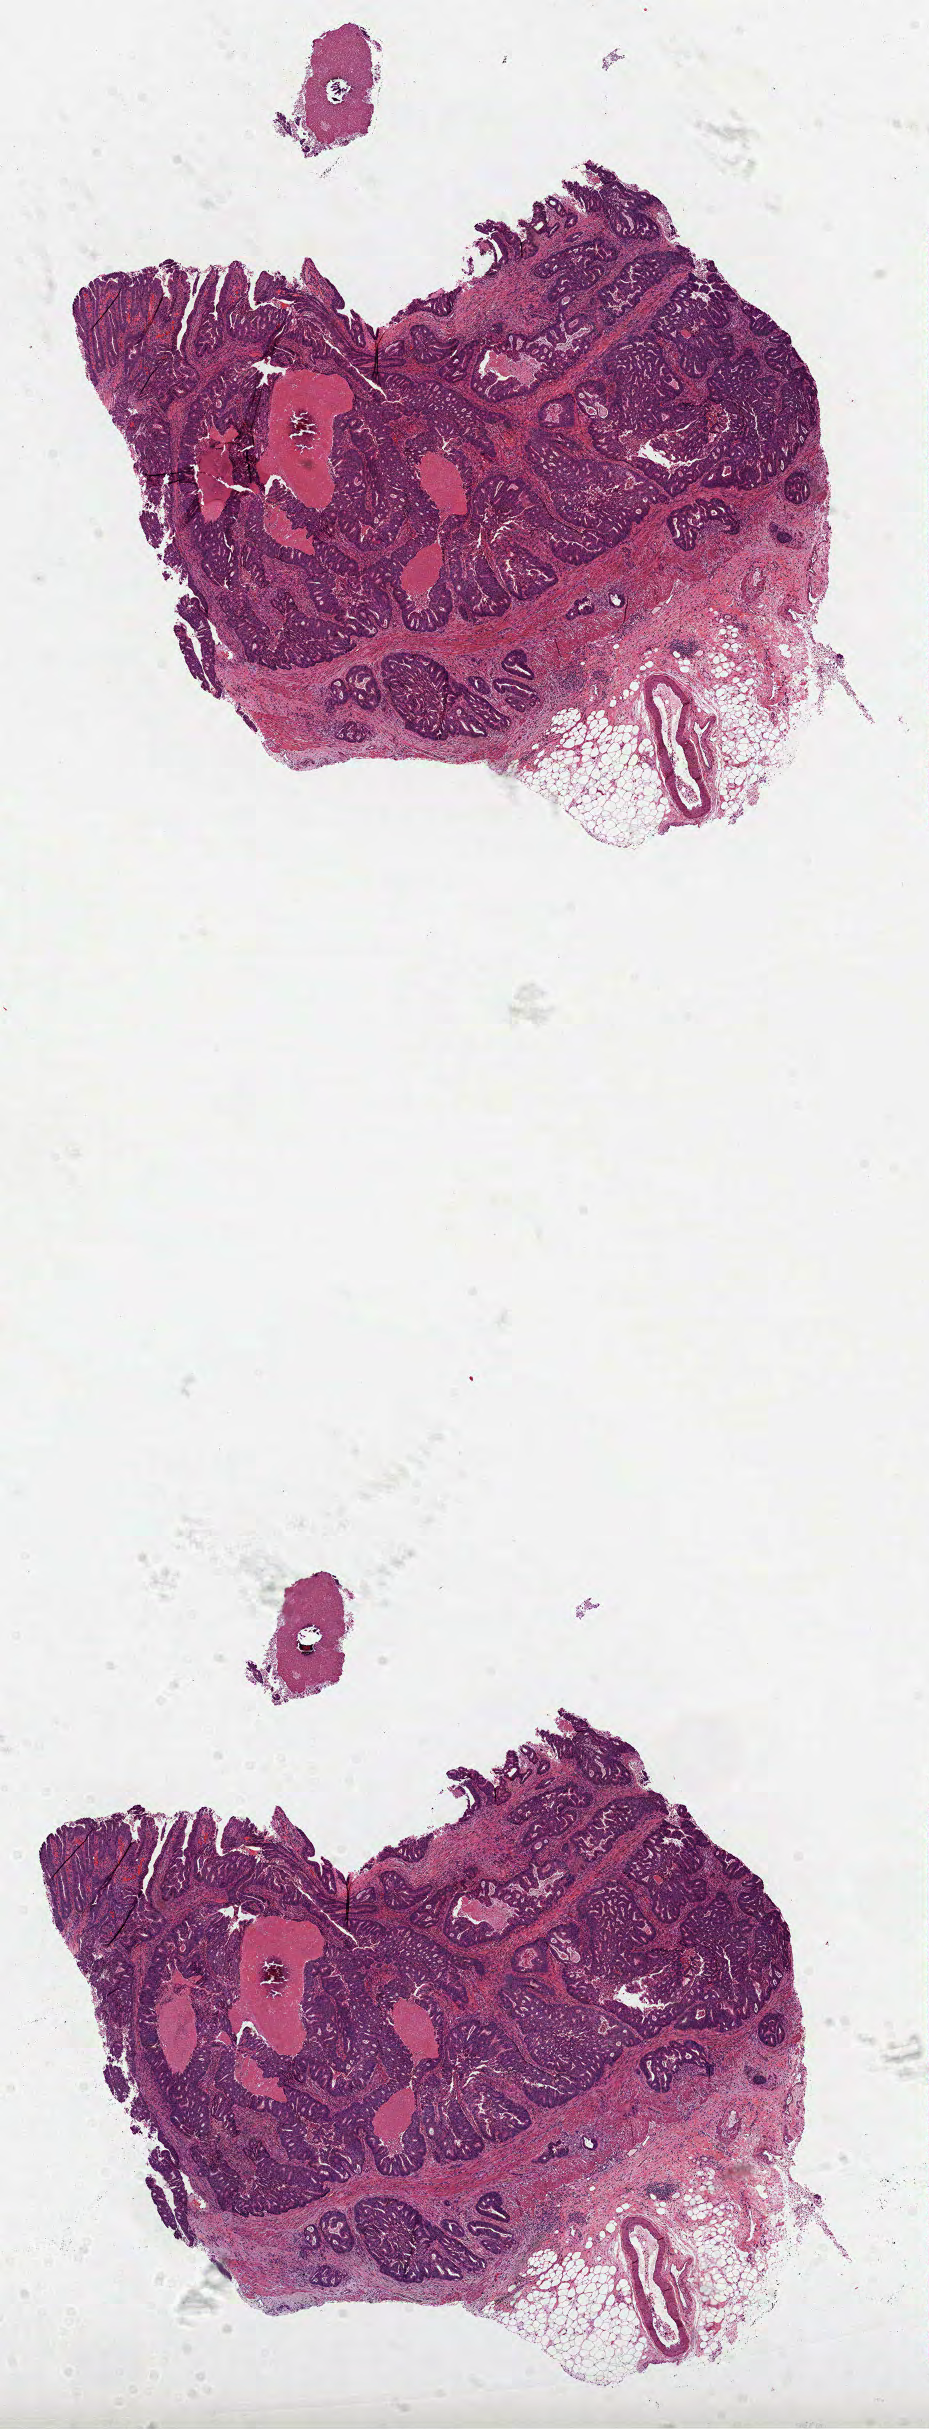
Whole-slide histology image, H&E, low-resolution overview of the scanned area, about 7.5 x 19.6 mm (from a 40x scan), formalin-fixed paraffin-embedded (FFPE) diagnostic section, primary tumour sample from the colon. Female patient; age at initial diagnosis 68 years.
TNM: T3 N2 M0. Histologic diagnosis: Adenocarcinoma, NOS (ascending colon). Lymph nodes positive (case pathology): 5 of 30 examined. AJCC pathologic stage: IIIC (6th edition).